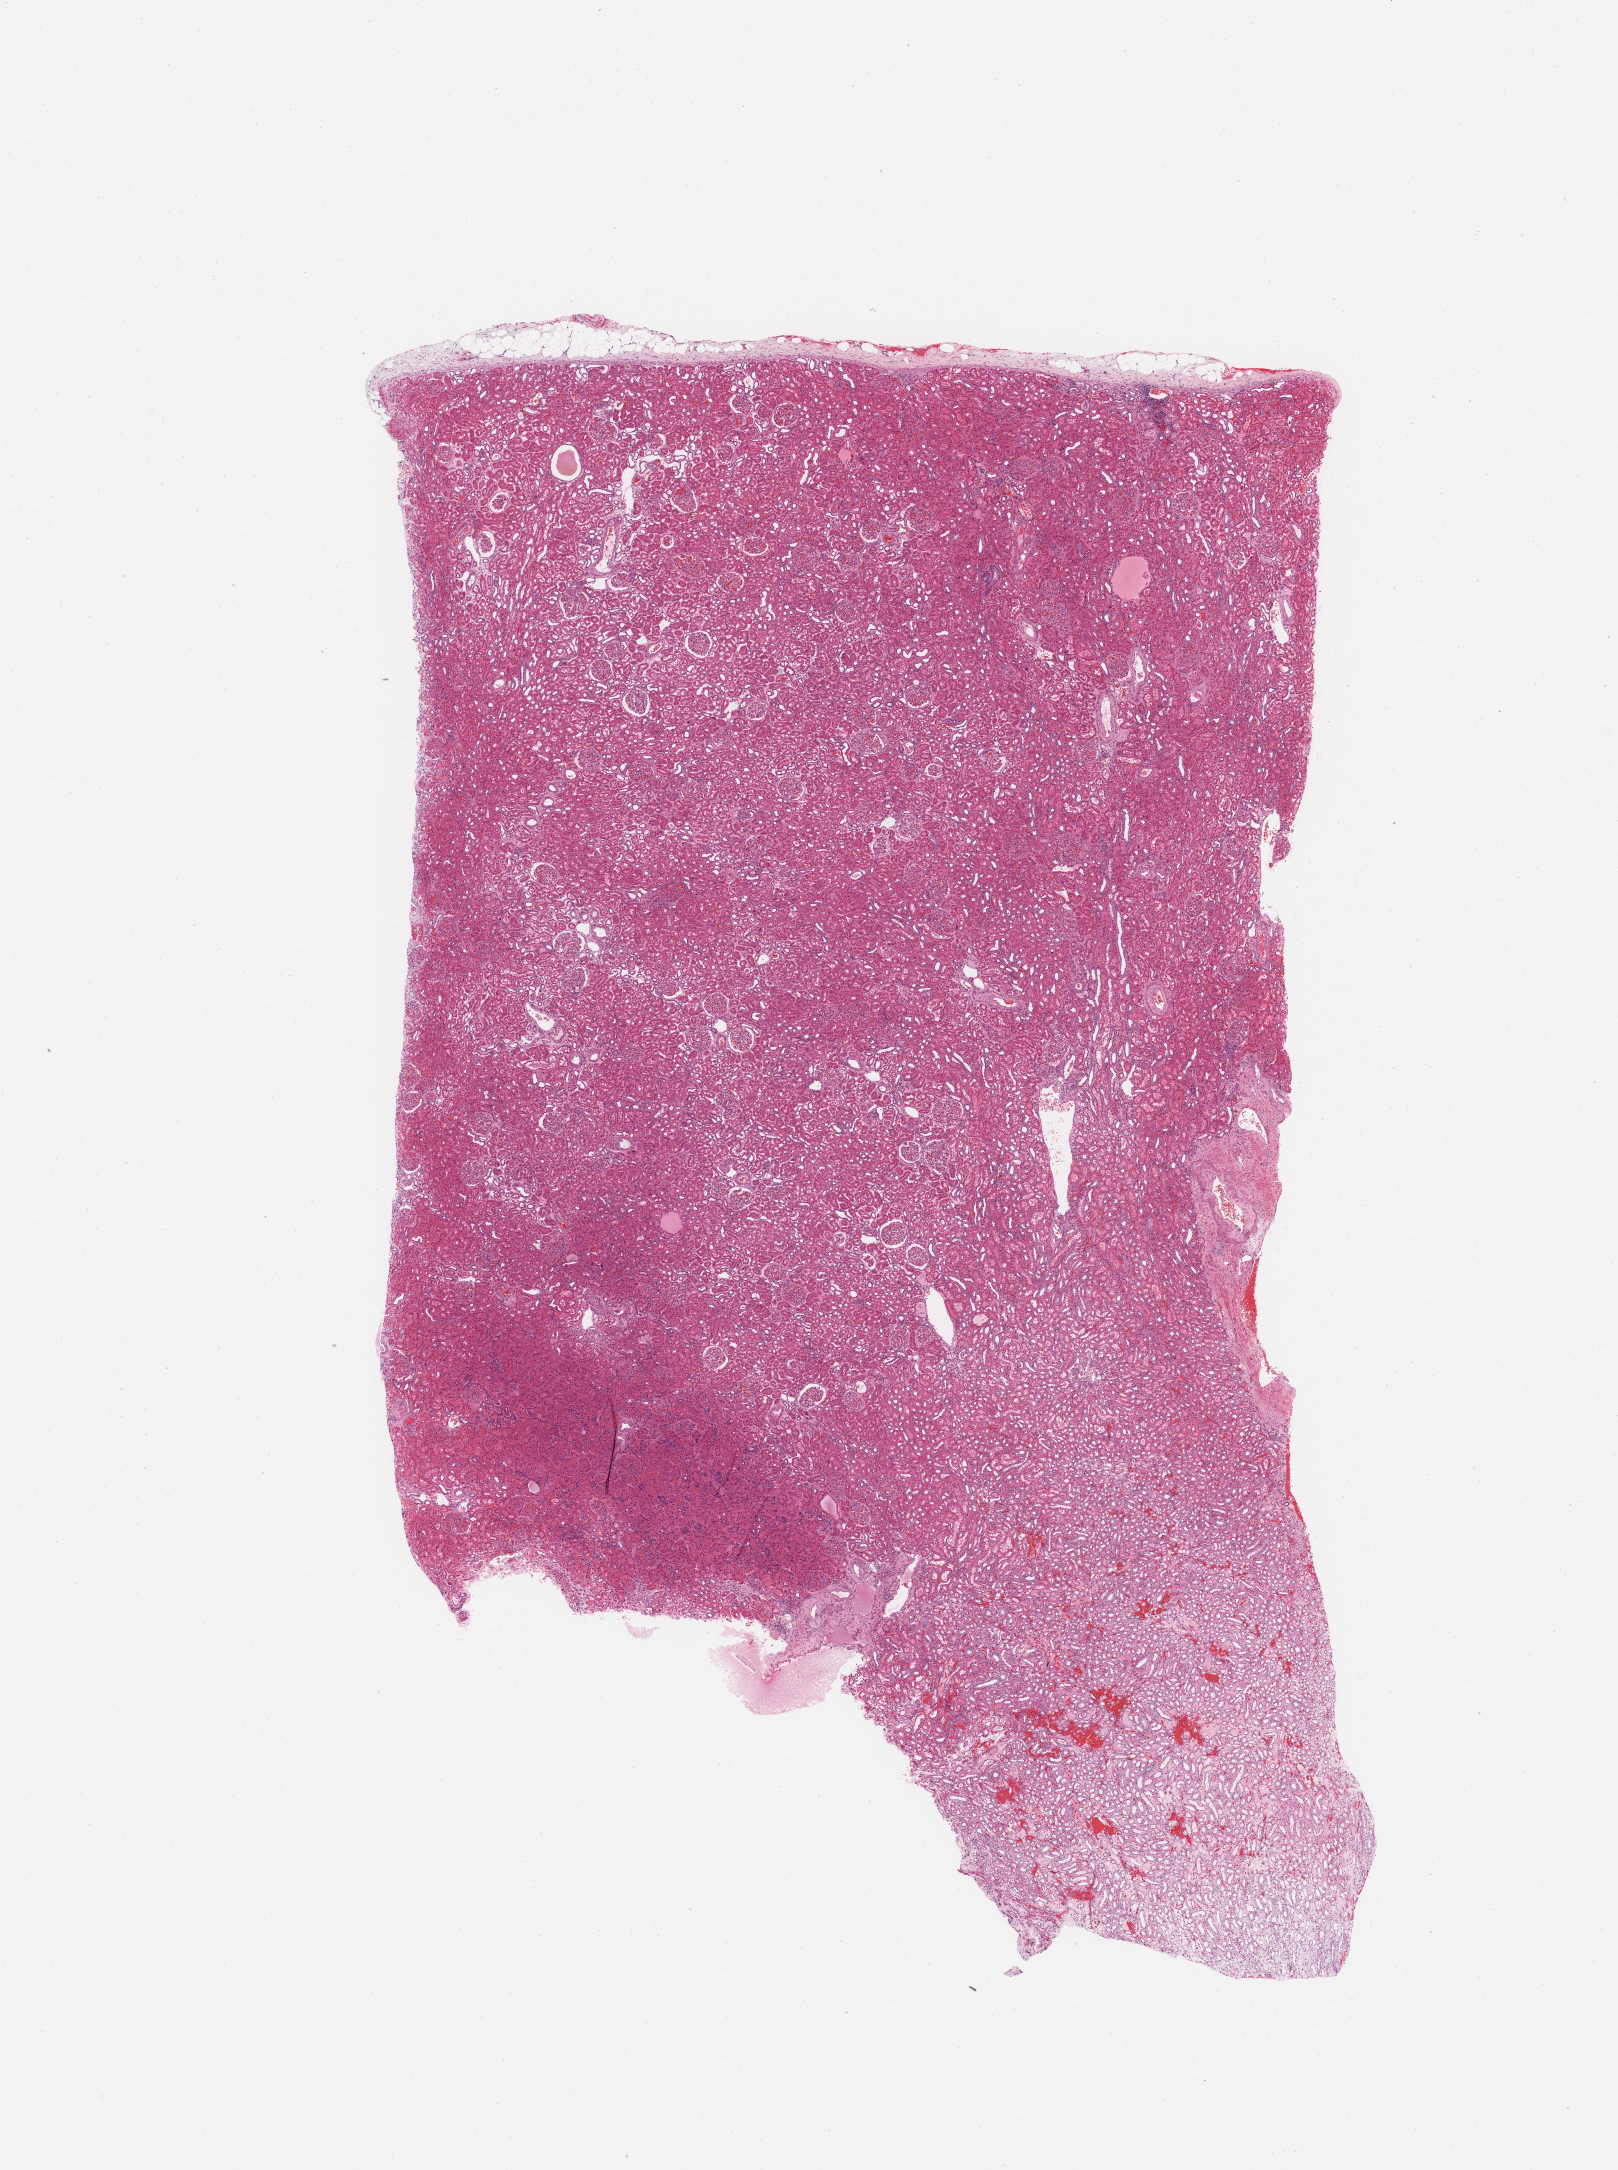
Whole-slide histology image, H&E, whole scanned area (about 12.8 x 17.2 mm, acquisition: 20x scan) shown as a low-resolution overview, normal (non-tumour) tissue sample, sampled site: kidney. Male, 55 y/o.
This section: normal (non-tumour) tissue from the same patient. Patient diagnosis: Renal cell carcinoma, NOS.